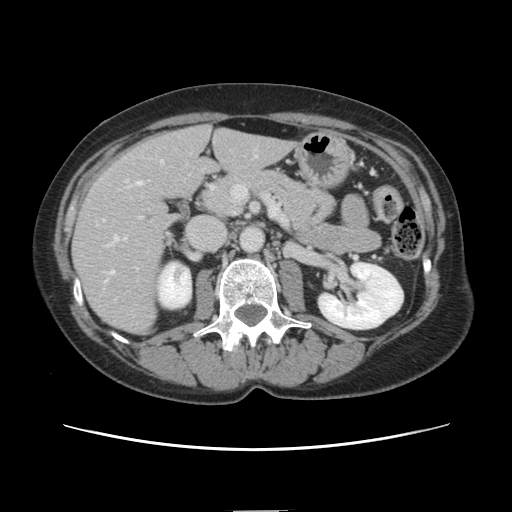
Contrast-enhanced abdominal CT, one axial slice; position 59 of 141 along the scan axis; 120 kVp; soft-tissue window (W 400 / L 40 HU); 2.5 mm slice thickness; 512 × 512 image matrix. Female patient, age 63 years. Case-level facts recorded for this patient, not image findings: diagnosis: colorectal cancer liver metastases, imaged before liver resection; multiple liver metastases: yes; largest metastasis: 3.2 cm; disease in both lobes: yes.
Structures marked on this image (manually delineated by an expert):
- hepatic veins: bounding box [x1, y1, x2, y2] px = [108, 181, 142, 277]
- liver: [74, 126, 292, 333]
- planned liver remnant (the part of the liver to remain after resection): [177, 126, 292, 187]
- portal vein (with intrahepatic branches): [114, 179, 133, 243]